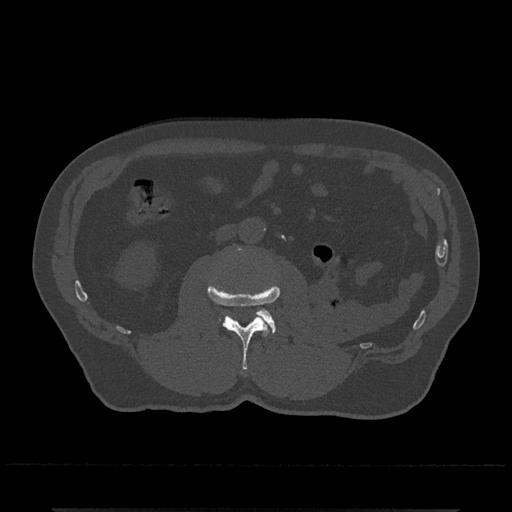
CT including the spine, one axial slice; slice 273 of 797 in the series (ordered by position); 120 kVp; bone window (W 1800 / L 400 HU); 0.5 mm slice thickness; 512 × 512 image matrix, field of view 393 × 393 mm. Patient: male, 67 years. From the clinical record (not read from this slice): primary cancer: prostate.
Outlined on this slice (semi-automatic segmentation, software-assisted and operator-edited):
- L2 vertebra: bounding box [x1, y1, x2, y2] px = [208, 248, 280, 370]
- L3 vertebra: [222, 309, 276, 334]